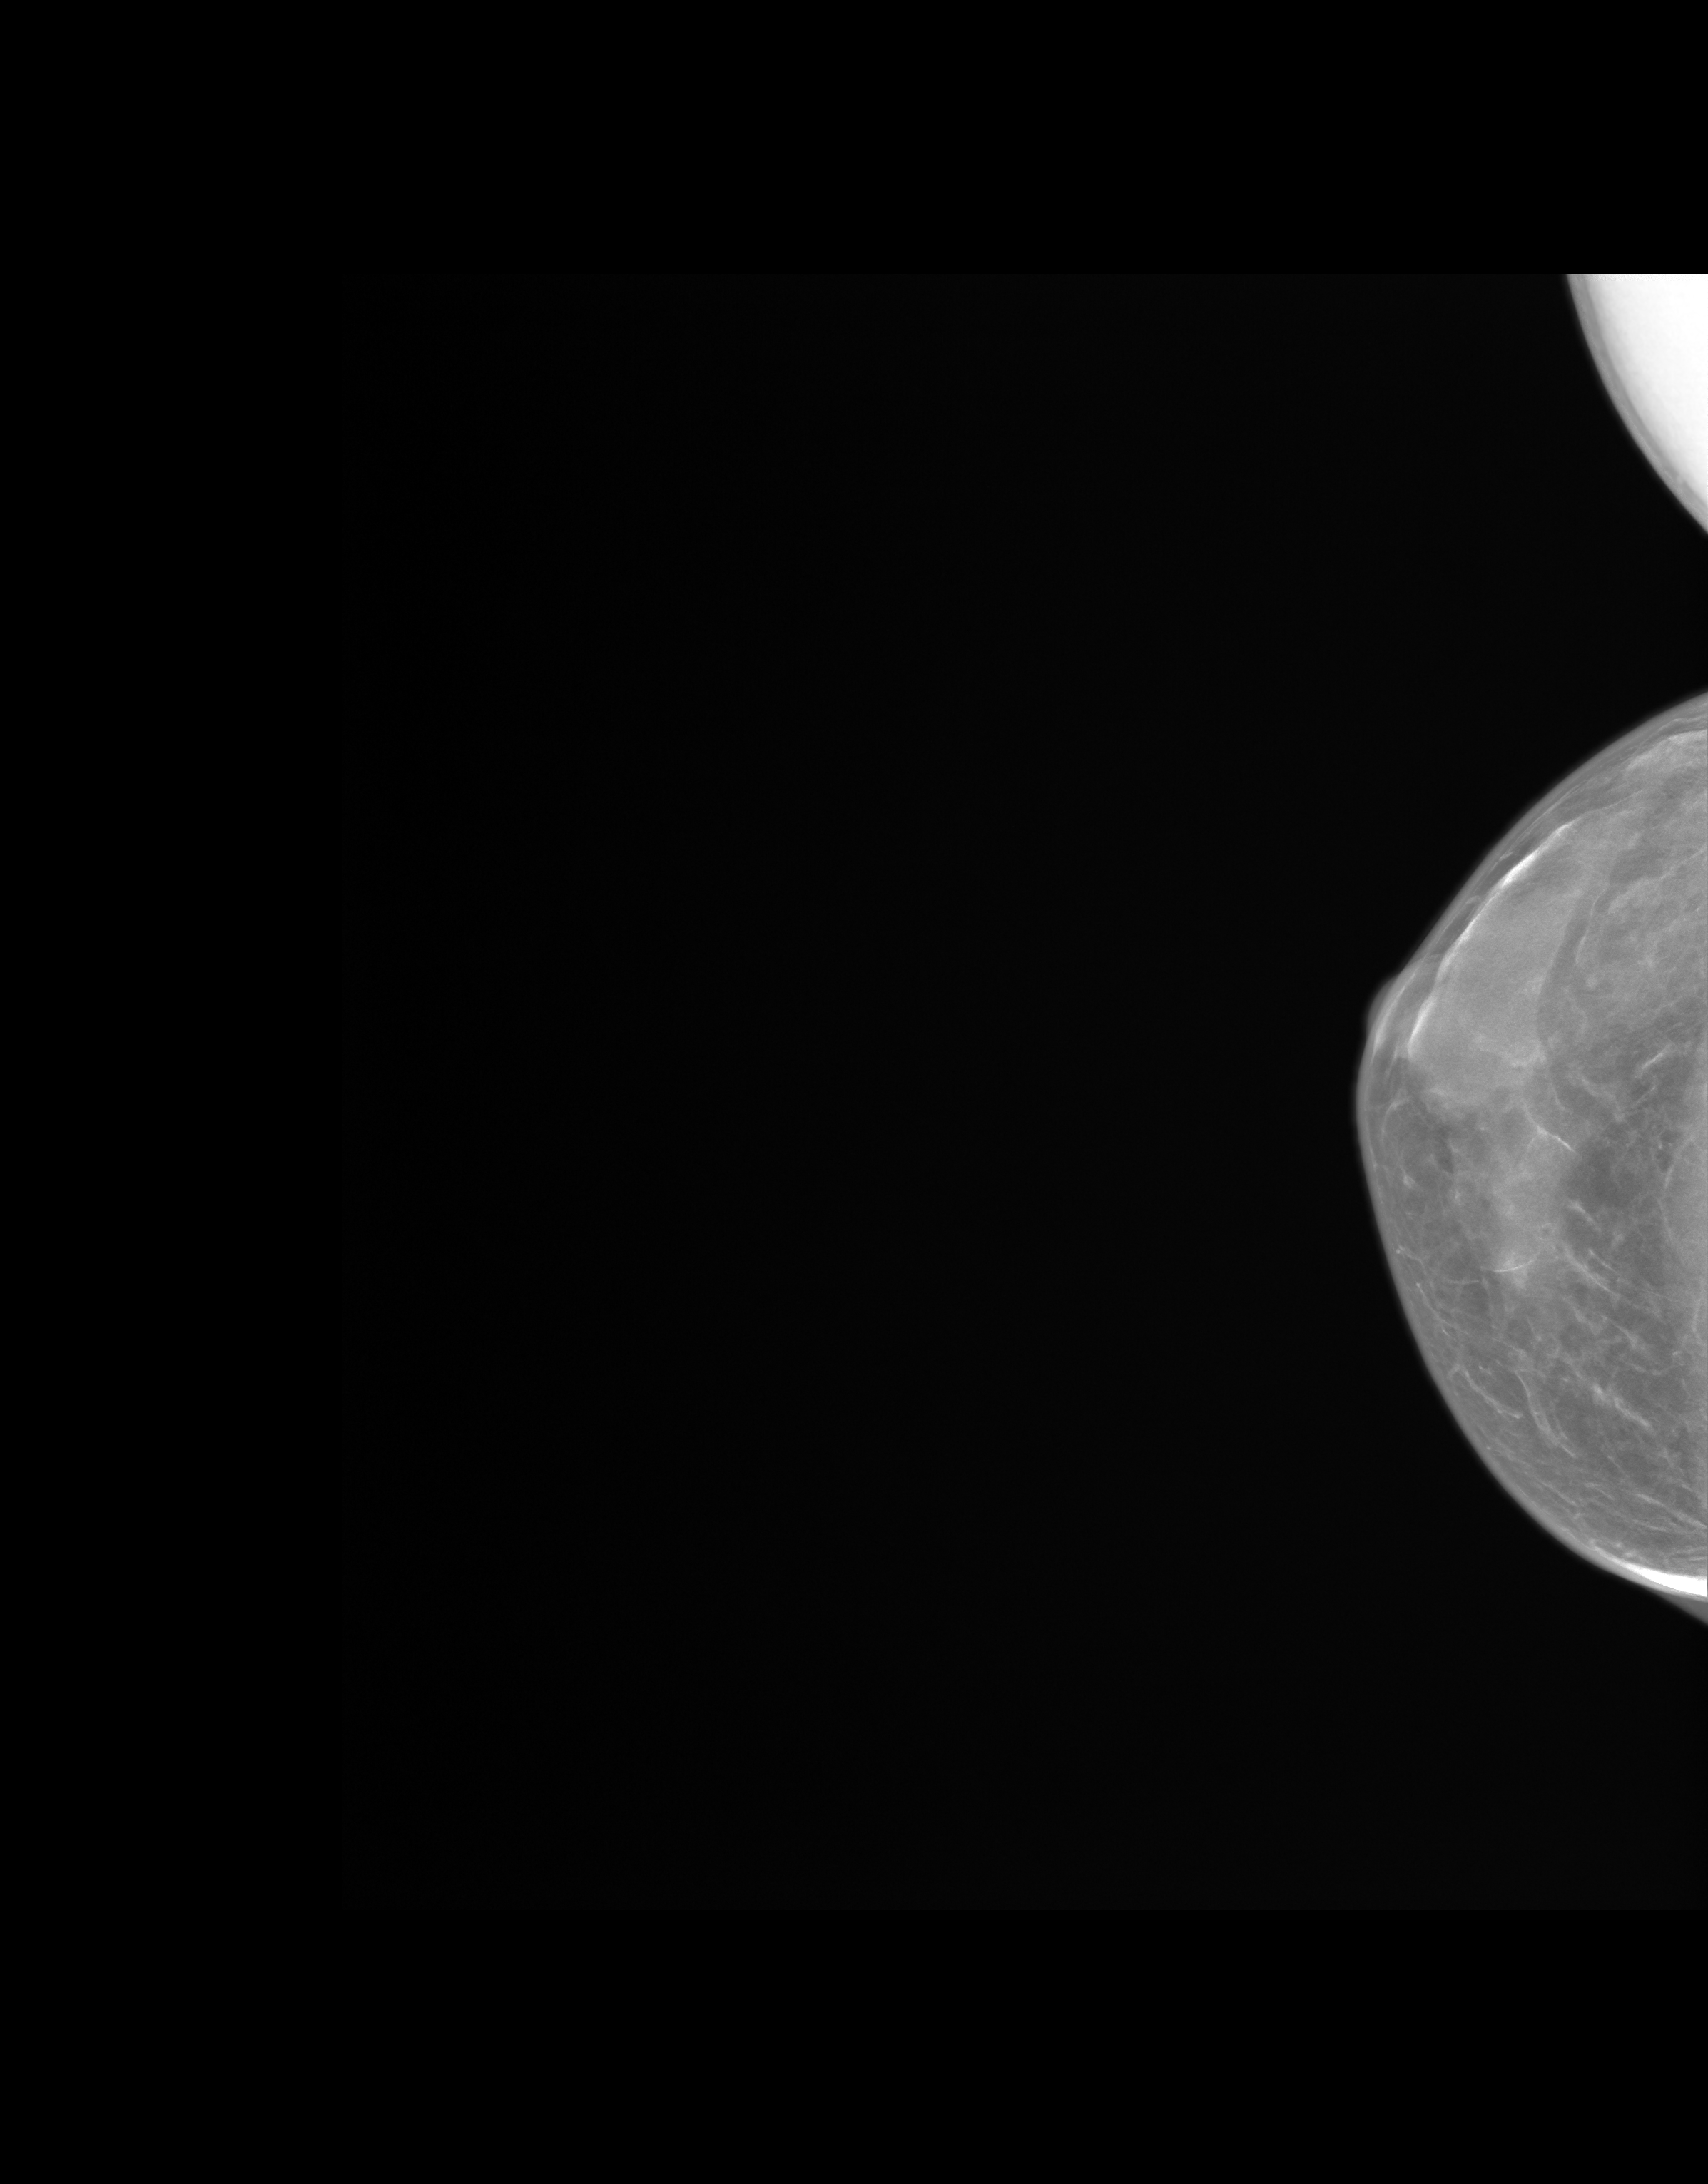
Synthetic 2-D view generated from a tomosynthesis acquisition (not an FFDM exposure); right breast; CC view; annual screening mammography examination. Female patient, age 55 years.
- breast density at the screening exam (both breasts): extremely dense (BI-RADS density category d)
- final BI-RADS category for the screening round (tomosynthesis exam, both breasts): category 1
- recall: no recall after this screen